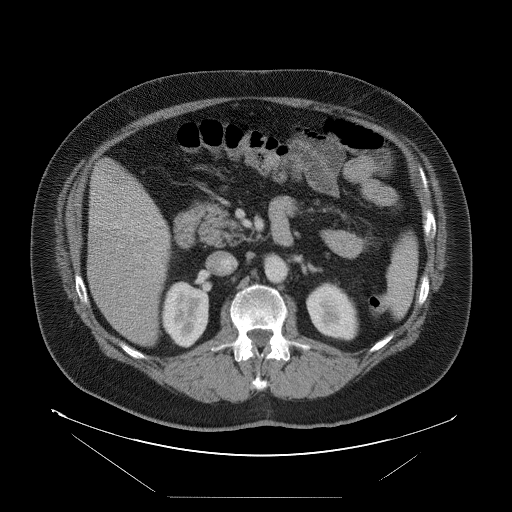
Contrast-enhanced abdominal CT, one axial slice. Slice 40 of 114 in the series (ordered by position). Intravenous contrast given. Soft-tissue window (W 400 / L 40 HU). 512 × 512 image matrix. Male patient, age 61 years. Case-level facts recorded for this patient, not image findings: diagnosis: colorectal cancer liver metastases, imaged before liver resection; multiple liver metastases: no.
Annotated regions visible in this slice (outlined manually by an expert reader):
- liver: bounding box [x1, y1, x2, y2] px = [89, 162, 171, 346]